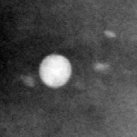
Crop from a digitized film mammogram around one marked abnormality, left breast, MLO view, BI-RADS breast density category 4 (scale 1–4).
- Marked abnormality: calcifications, morphology round and regular / lucent center / punctate, distribution diffusely scattered; BI-RADS assessment category 2; subtlety rating 5 on a 1 (subtle) to 5 (obvious) scale; benign; no additional work-up was recommended (benign without callback).